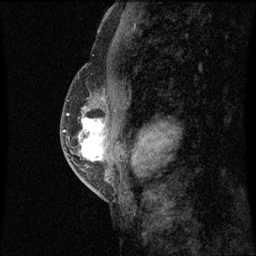
Breast MRI (dynamic contrast-enhanced), one sagittal slice; dynamic contrast-enhanced series, image 2 of 3 at this slice position (ordered by acquisition); 1.5 T; TE 4.2 ms, TR 8.9 ms; 2 mm slice thickness; 256 × 256 image matrix, field of view 200 × 200 mm. Patient: female, 50 years. From the clinical record (not read from this slice): setting: breast cancer imaged before/during neoadjuvant chemotherapy; receptor status: triple-negative.
Structures marked on this image (semi-automatically segmented with operator editing):
- analysis volume of interest (the breast-tissue region the enhancement analysis was run in; not a lesion): bounding box (x1, y1, x2, y2) in pixels: (68, 82, 107, 169)
- tumour enhancement mask (voxels above the 70 % enhancement threshold inside the analysis volume of interest): (82, 118, 104, 161)